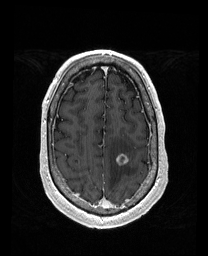
Brain MRI from a brain-tumour surgery series, one axial slice; slice 139 of 192 in the series (ordered by position); T1-weighted post-contrast; 208 × 256 image matrix, field of view 211 × 260 mm. Case-level facts recorded for this patient, not image findings: histopathology: Metastatic Carcinoma from Lung Adenocarcinoma; tumour location: Left Frontal.
Structures marked on this image (outlined manually by an expert reader):
- tumour: box from (x=116, y=154) to (x=128, y=165) px